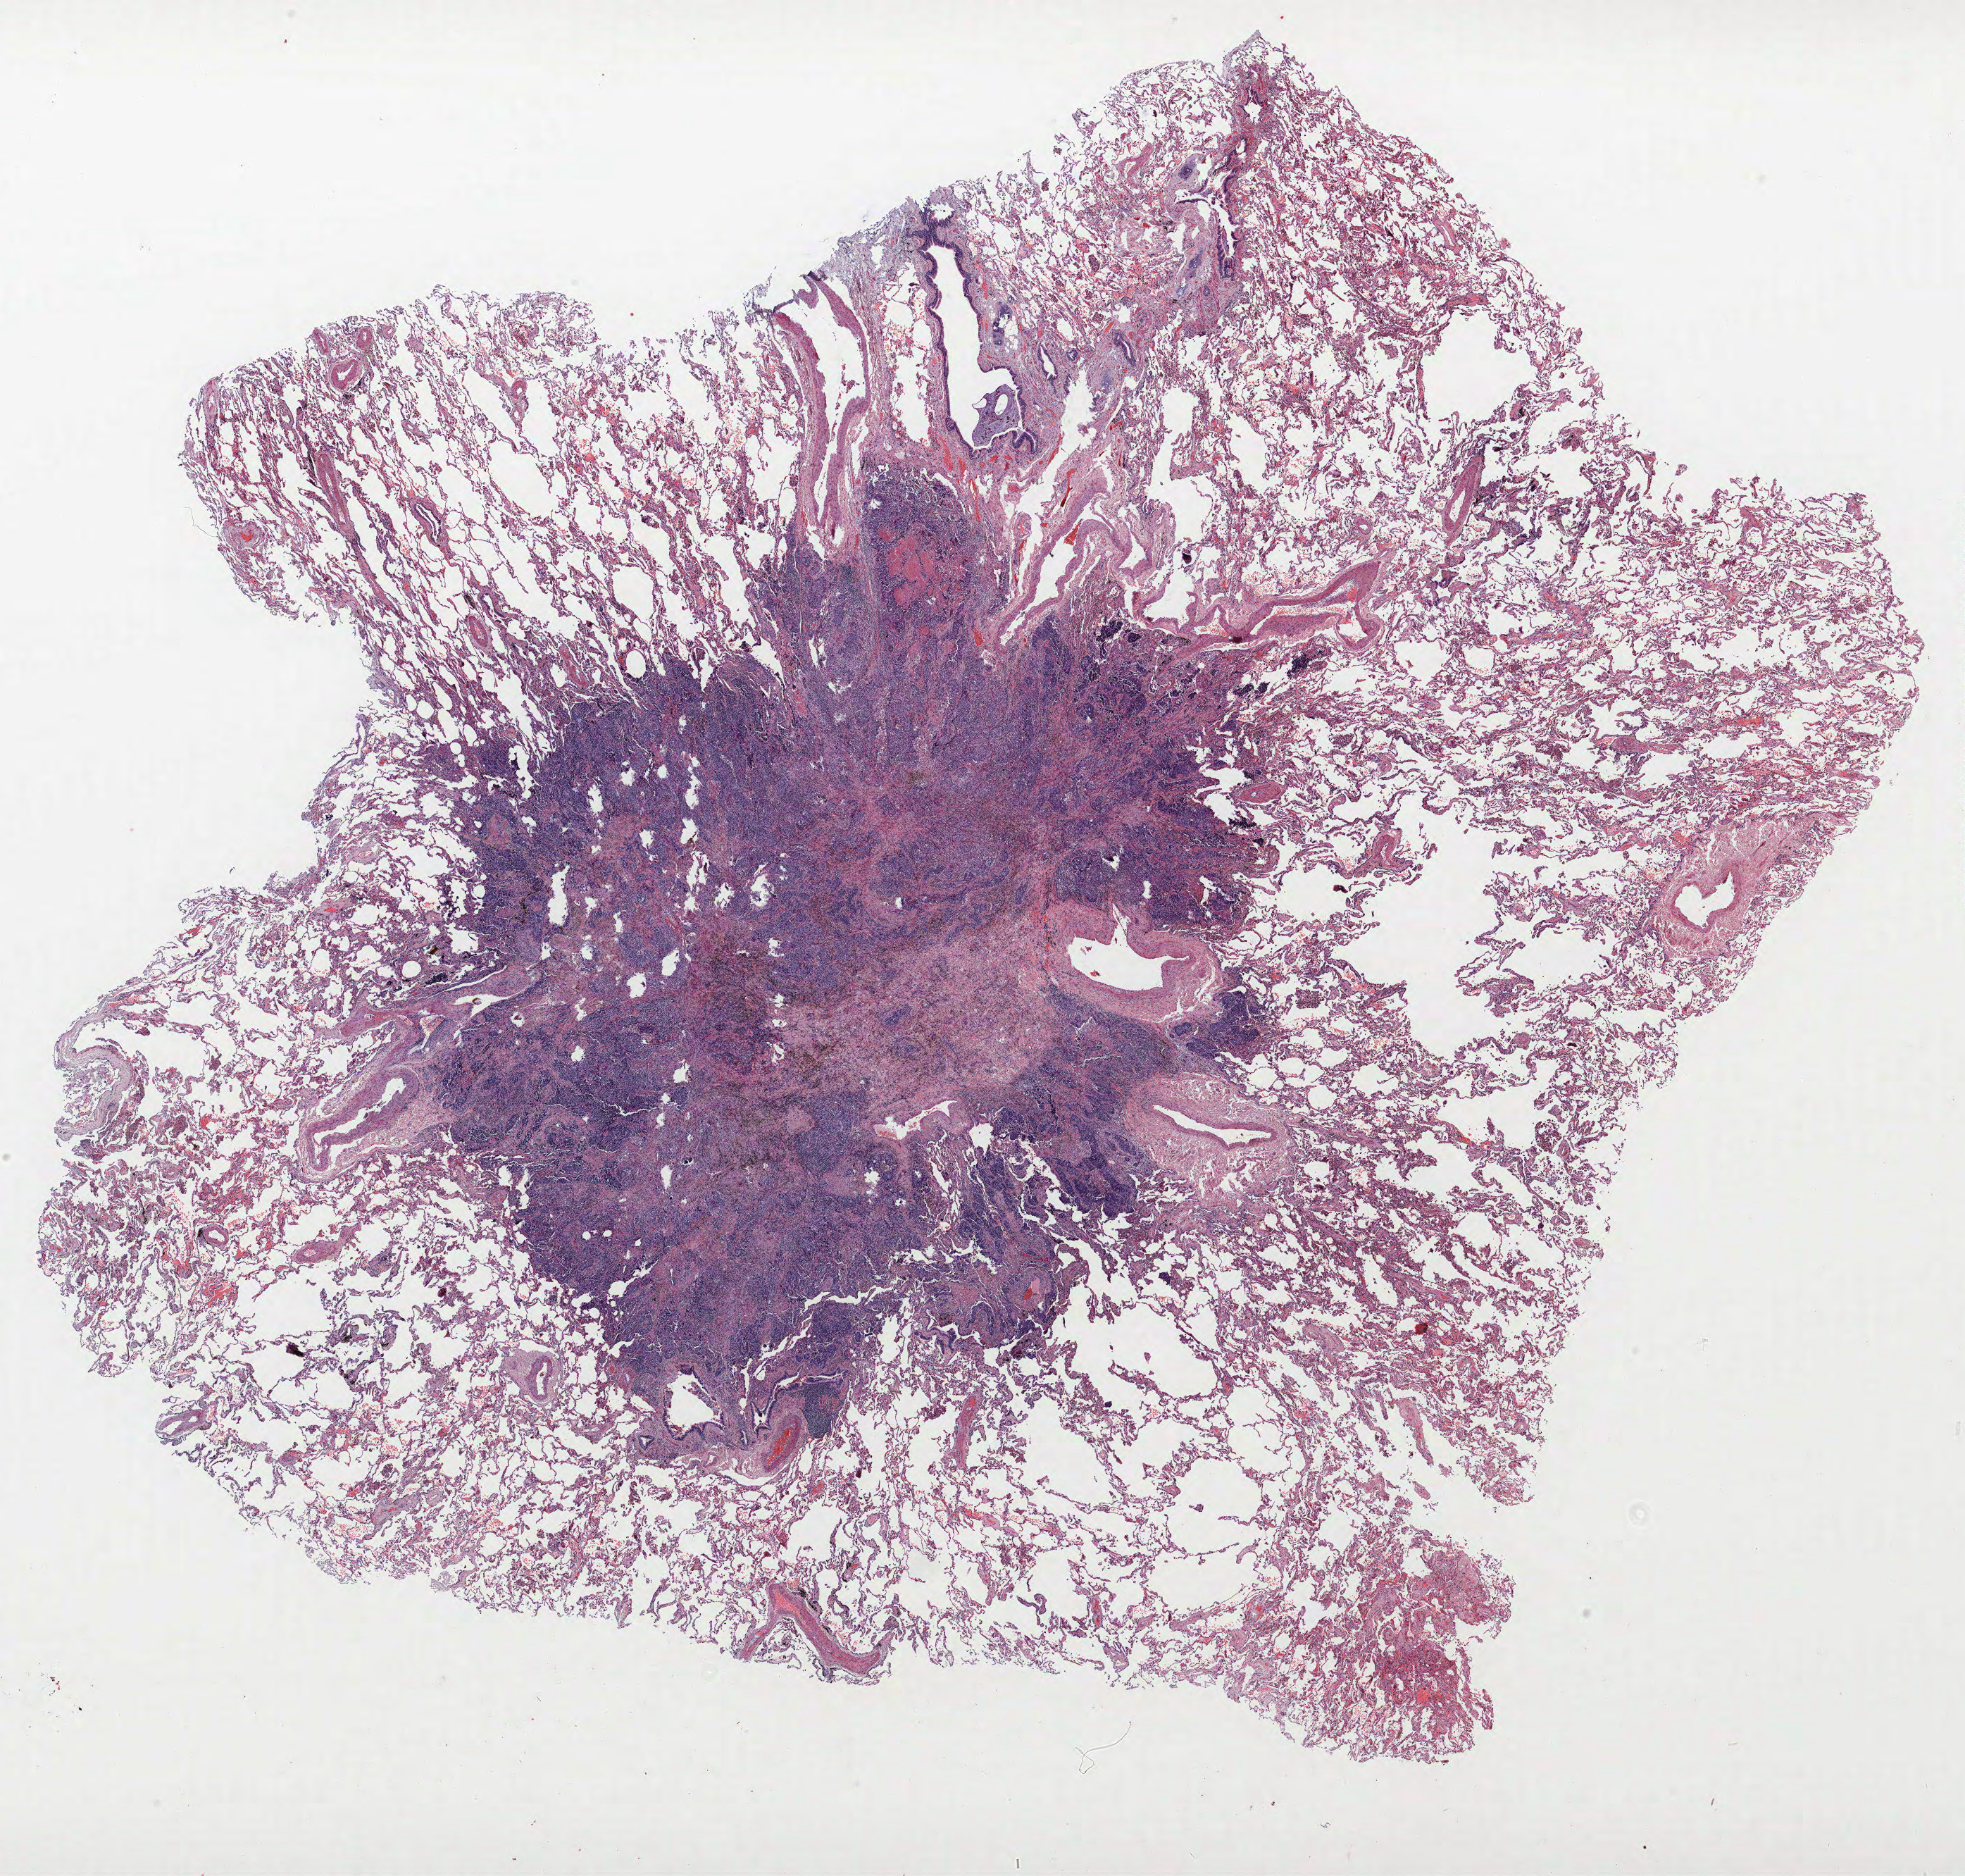
Whole-slide histology image, Hematoxylin and eosin (H&E) stained — low-resolution overview of the scanned area, about 22.3 x 21.3 mm (slide scanned at 40x), formalin-fixed paraffin-embedded (FFPE) section, lung. Male, age 64 at enrolment. Current smoker at enrolment. Grade: poorly differentiated (G3).
- stage (AJCC 6th edition): IA
- tumour size (pathology): 10 mm
- ICD-O-3 topography: upper lobe of lung (C34.1)
- primary tumour location (clinical record): left upper lobe
- participant's lung-cancer diagnosis: Adenocarcinoma, NOS